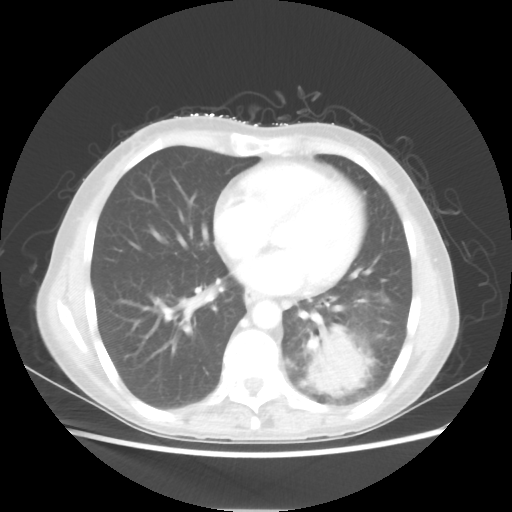
Chest CT, one axial slice; position 23 of 56 along the scan axis; lung window (W 1500 / L -600 HU); 512 × 512 image matrix, field of view 360 × 360 mm. Patient: female, 53 years. From the clinical record (not read from this slice): clinical TNM (as recorded): T3 N0 M0.
Outlined on this slice (rectangle marked by the reading radiologist):
- lung tumour (recorded histology: adenocarcinoma): box from (x=305, y=326) to (x=372, y=396) px